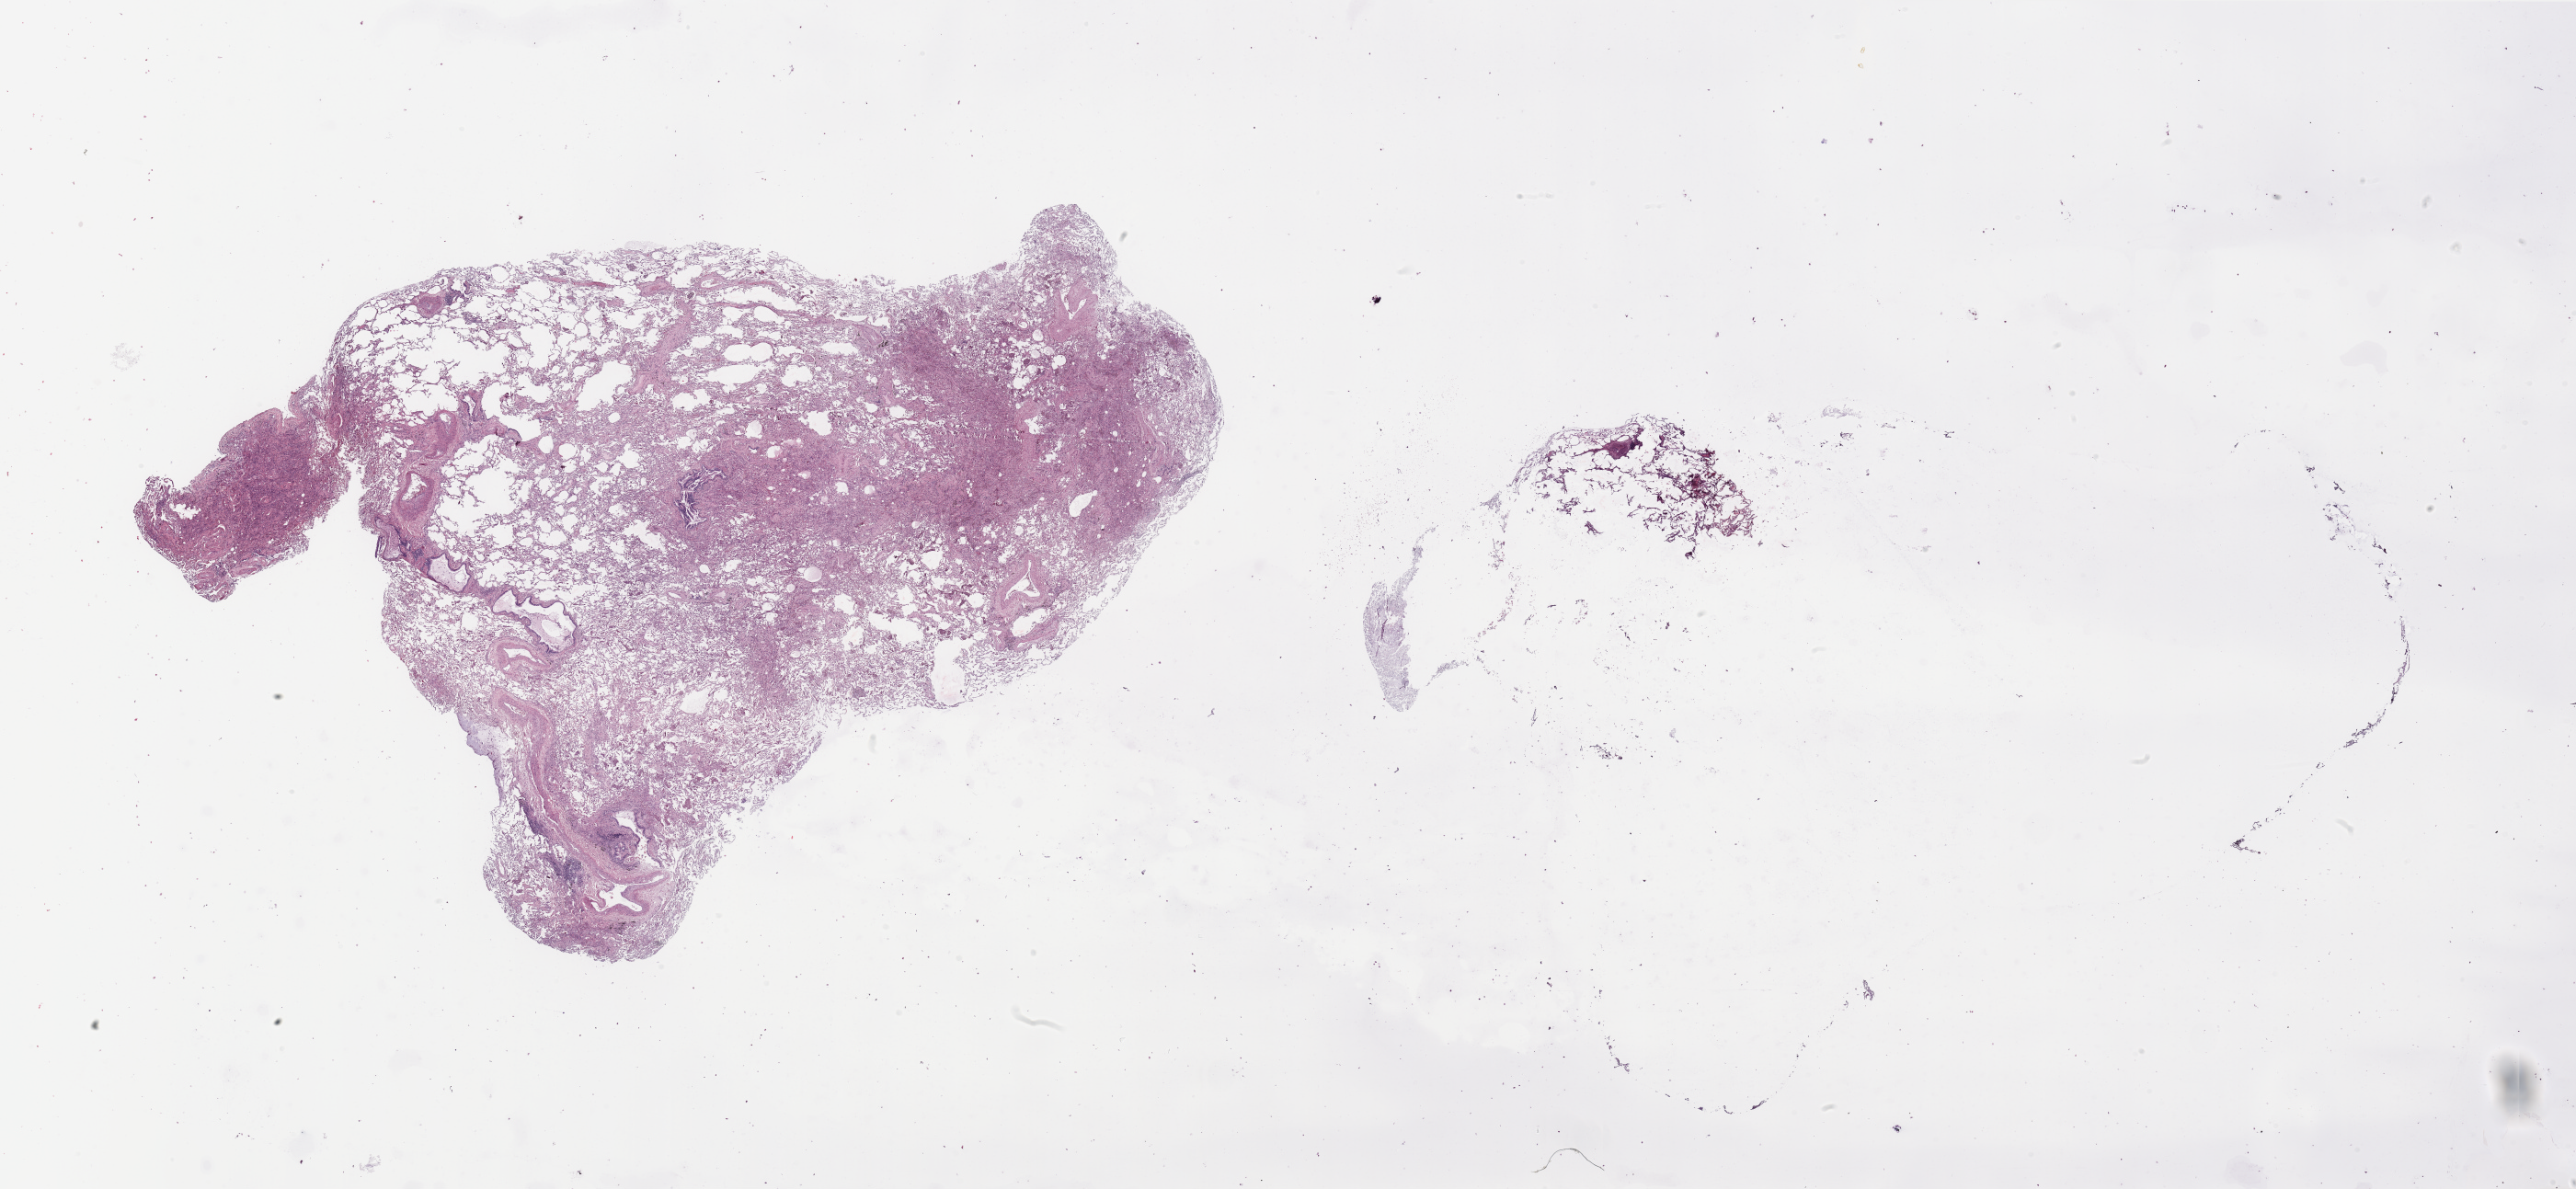
H&E-stained whole-slide image, a low-resolution overview of the entire scanned area, about 44.3 x 20.4 mm (from a 20x scan); normal (non-tumour) tissue sample, lung. Male, 61 y/o.
• this section: normal (non-tumour) tissue from the same patient
• patient diagnosis: Squamous cell carcinoma, NOS